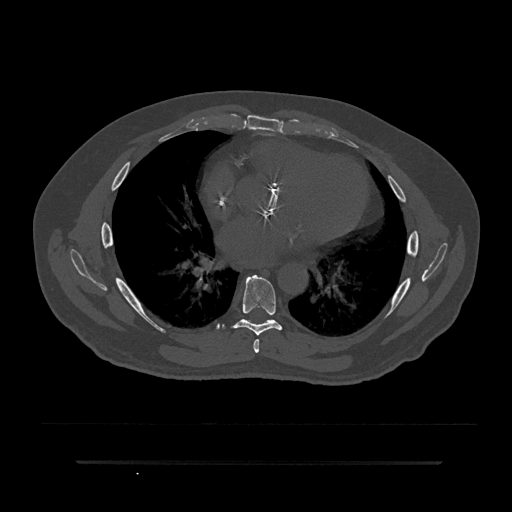
CT including the spine, one axial slice. Slice 480 of 797 in the series (ordered by position). Reconstruction kernel Br40s/3. Bone window (W 1800 / L 400 HU). 512 × 512 image matrix, field of view 464 × 464 mm. Male patient, age 59 years. From the clinical record (not read from this slice): primary cancer: bile ducts; vertebrae with lytic lesions (as recorded): T10.
Annotated regions visible in this slice (semi-automatically segmented with operator editing):
- T6 vertebra: bounding box <253,339,260,353> (left, top, right, bottom; pixels)
- T7 vertebra: <232,275,283,336>